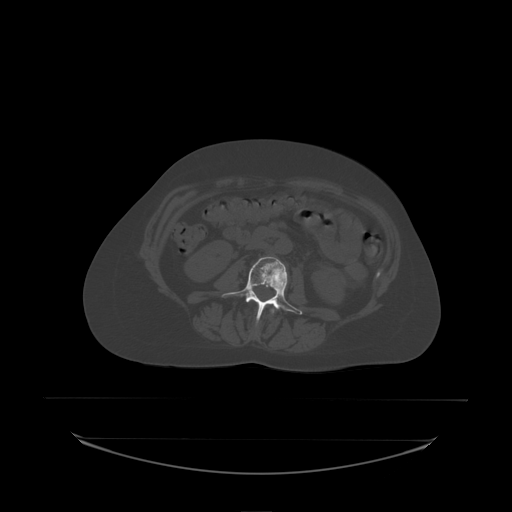
CT including the spine, one axial slice. Position 62 of 242 along the scan axis. Bone window (W 1800 / L 400 HU). 2.5 mm slice thickness. 512 × 512 image matrix, field of view 500 × 500 mm. Patient: female, 53 years. From the clinical record (not read from this slice): primary cancer: lung; vertebrae with lytic lesions (as recorded): T7, L1.
Structures marked on this image (semi-automatic segmentation, software-assisted and operator-edited):
- L2 vertebra: bounding box (x1, y1, x2, y2) in pixels: (271, 309, 275, 314)
- L3 vertebra: (222, 257, 303, 323)